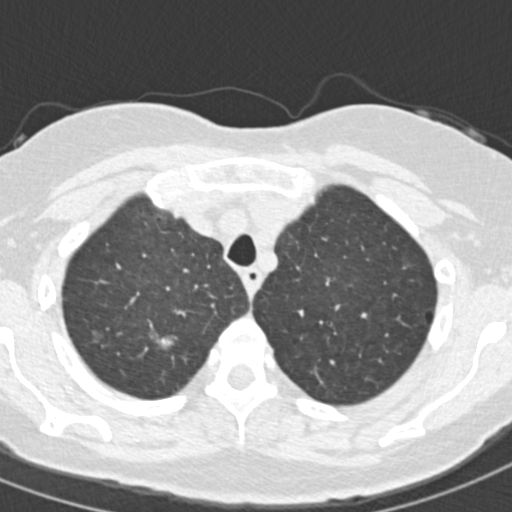
Low-dose screening chest CT, one axial slice. Slice 126 of 157 in the series (ordered by position). Lung window (W 1500 / L -600 HU). 2 mm slice thickness. 512 × 512 image matrix, field of view 280 × 280 mm.
Structures marked on this image (outlined manually by an expert reader):
- lesion 1 (tumor, upper lobe of right lung): bounding box (x1, y1, x2, y2) in pixels: (147, 318, 178, 350)